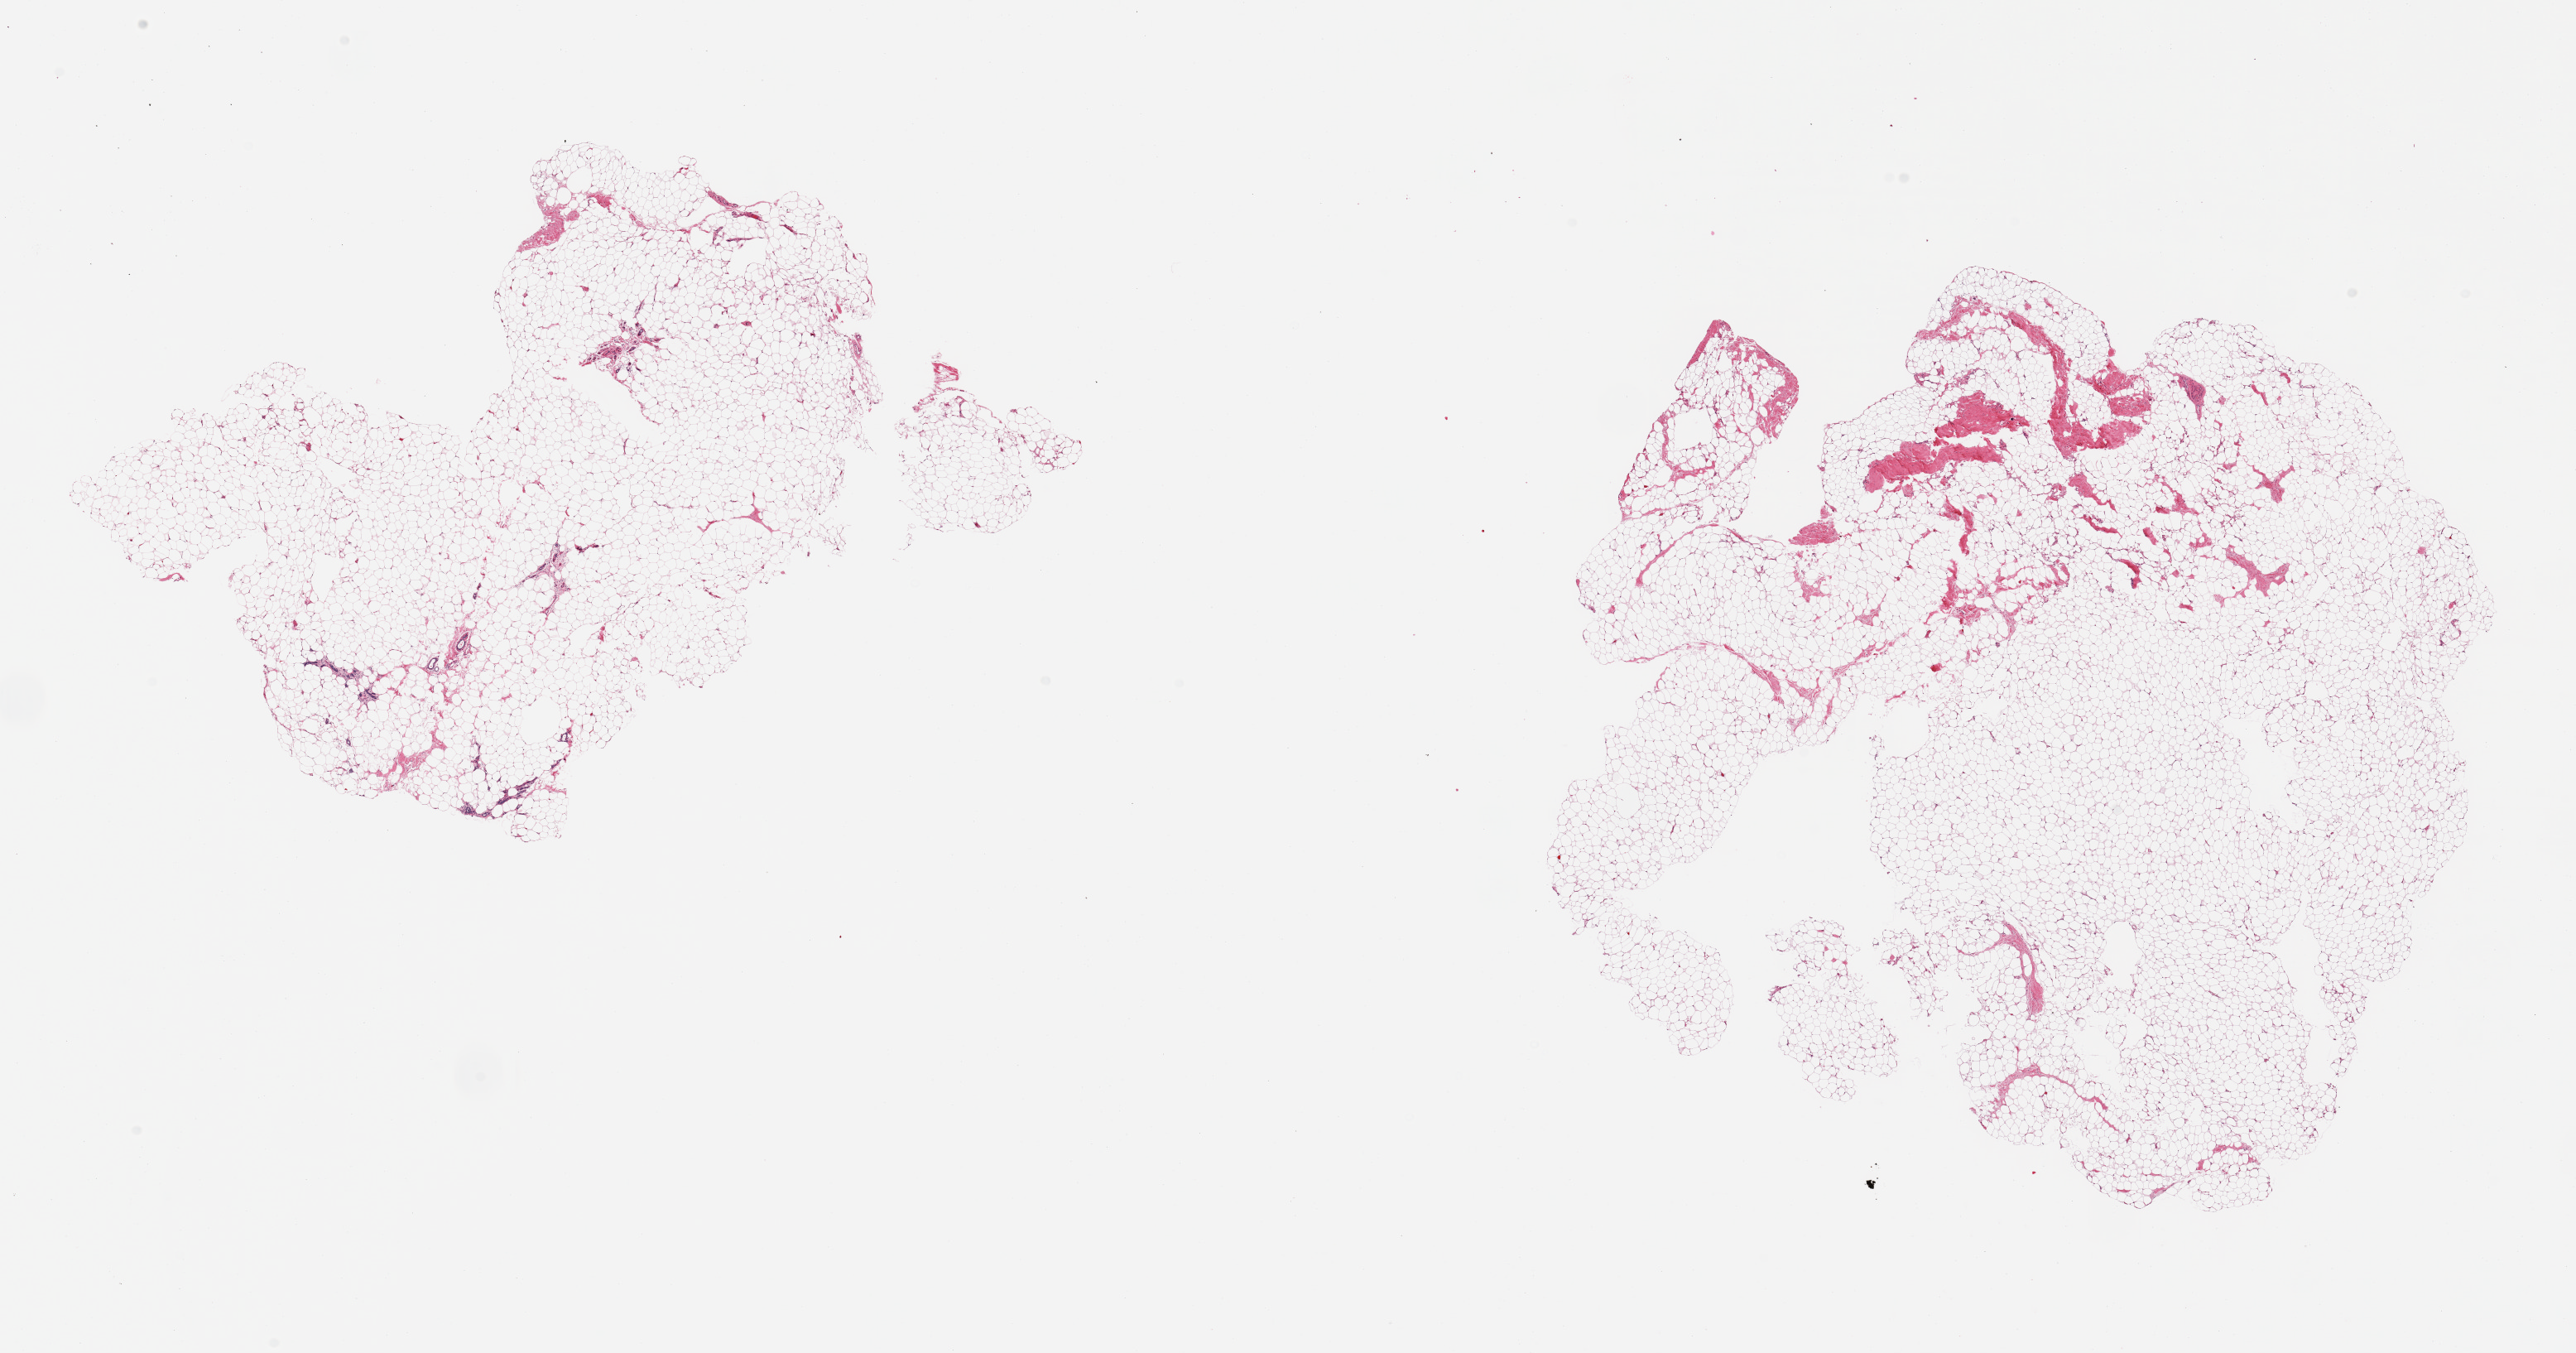
Whole-slide image, haematoxylin and eosin stain, low-resolution overview of the scanned area, about 24.6 x 12.9 mm. PAXgene-fixed, paraffin-embedded tissue. Section of breast (target tissue). Donor tissue sample. Donor: female.
Reviewer comment on this tissue sample: 2 pieces; atrophic ducts confined to 1 piece; fat comprises >95%.